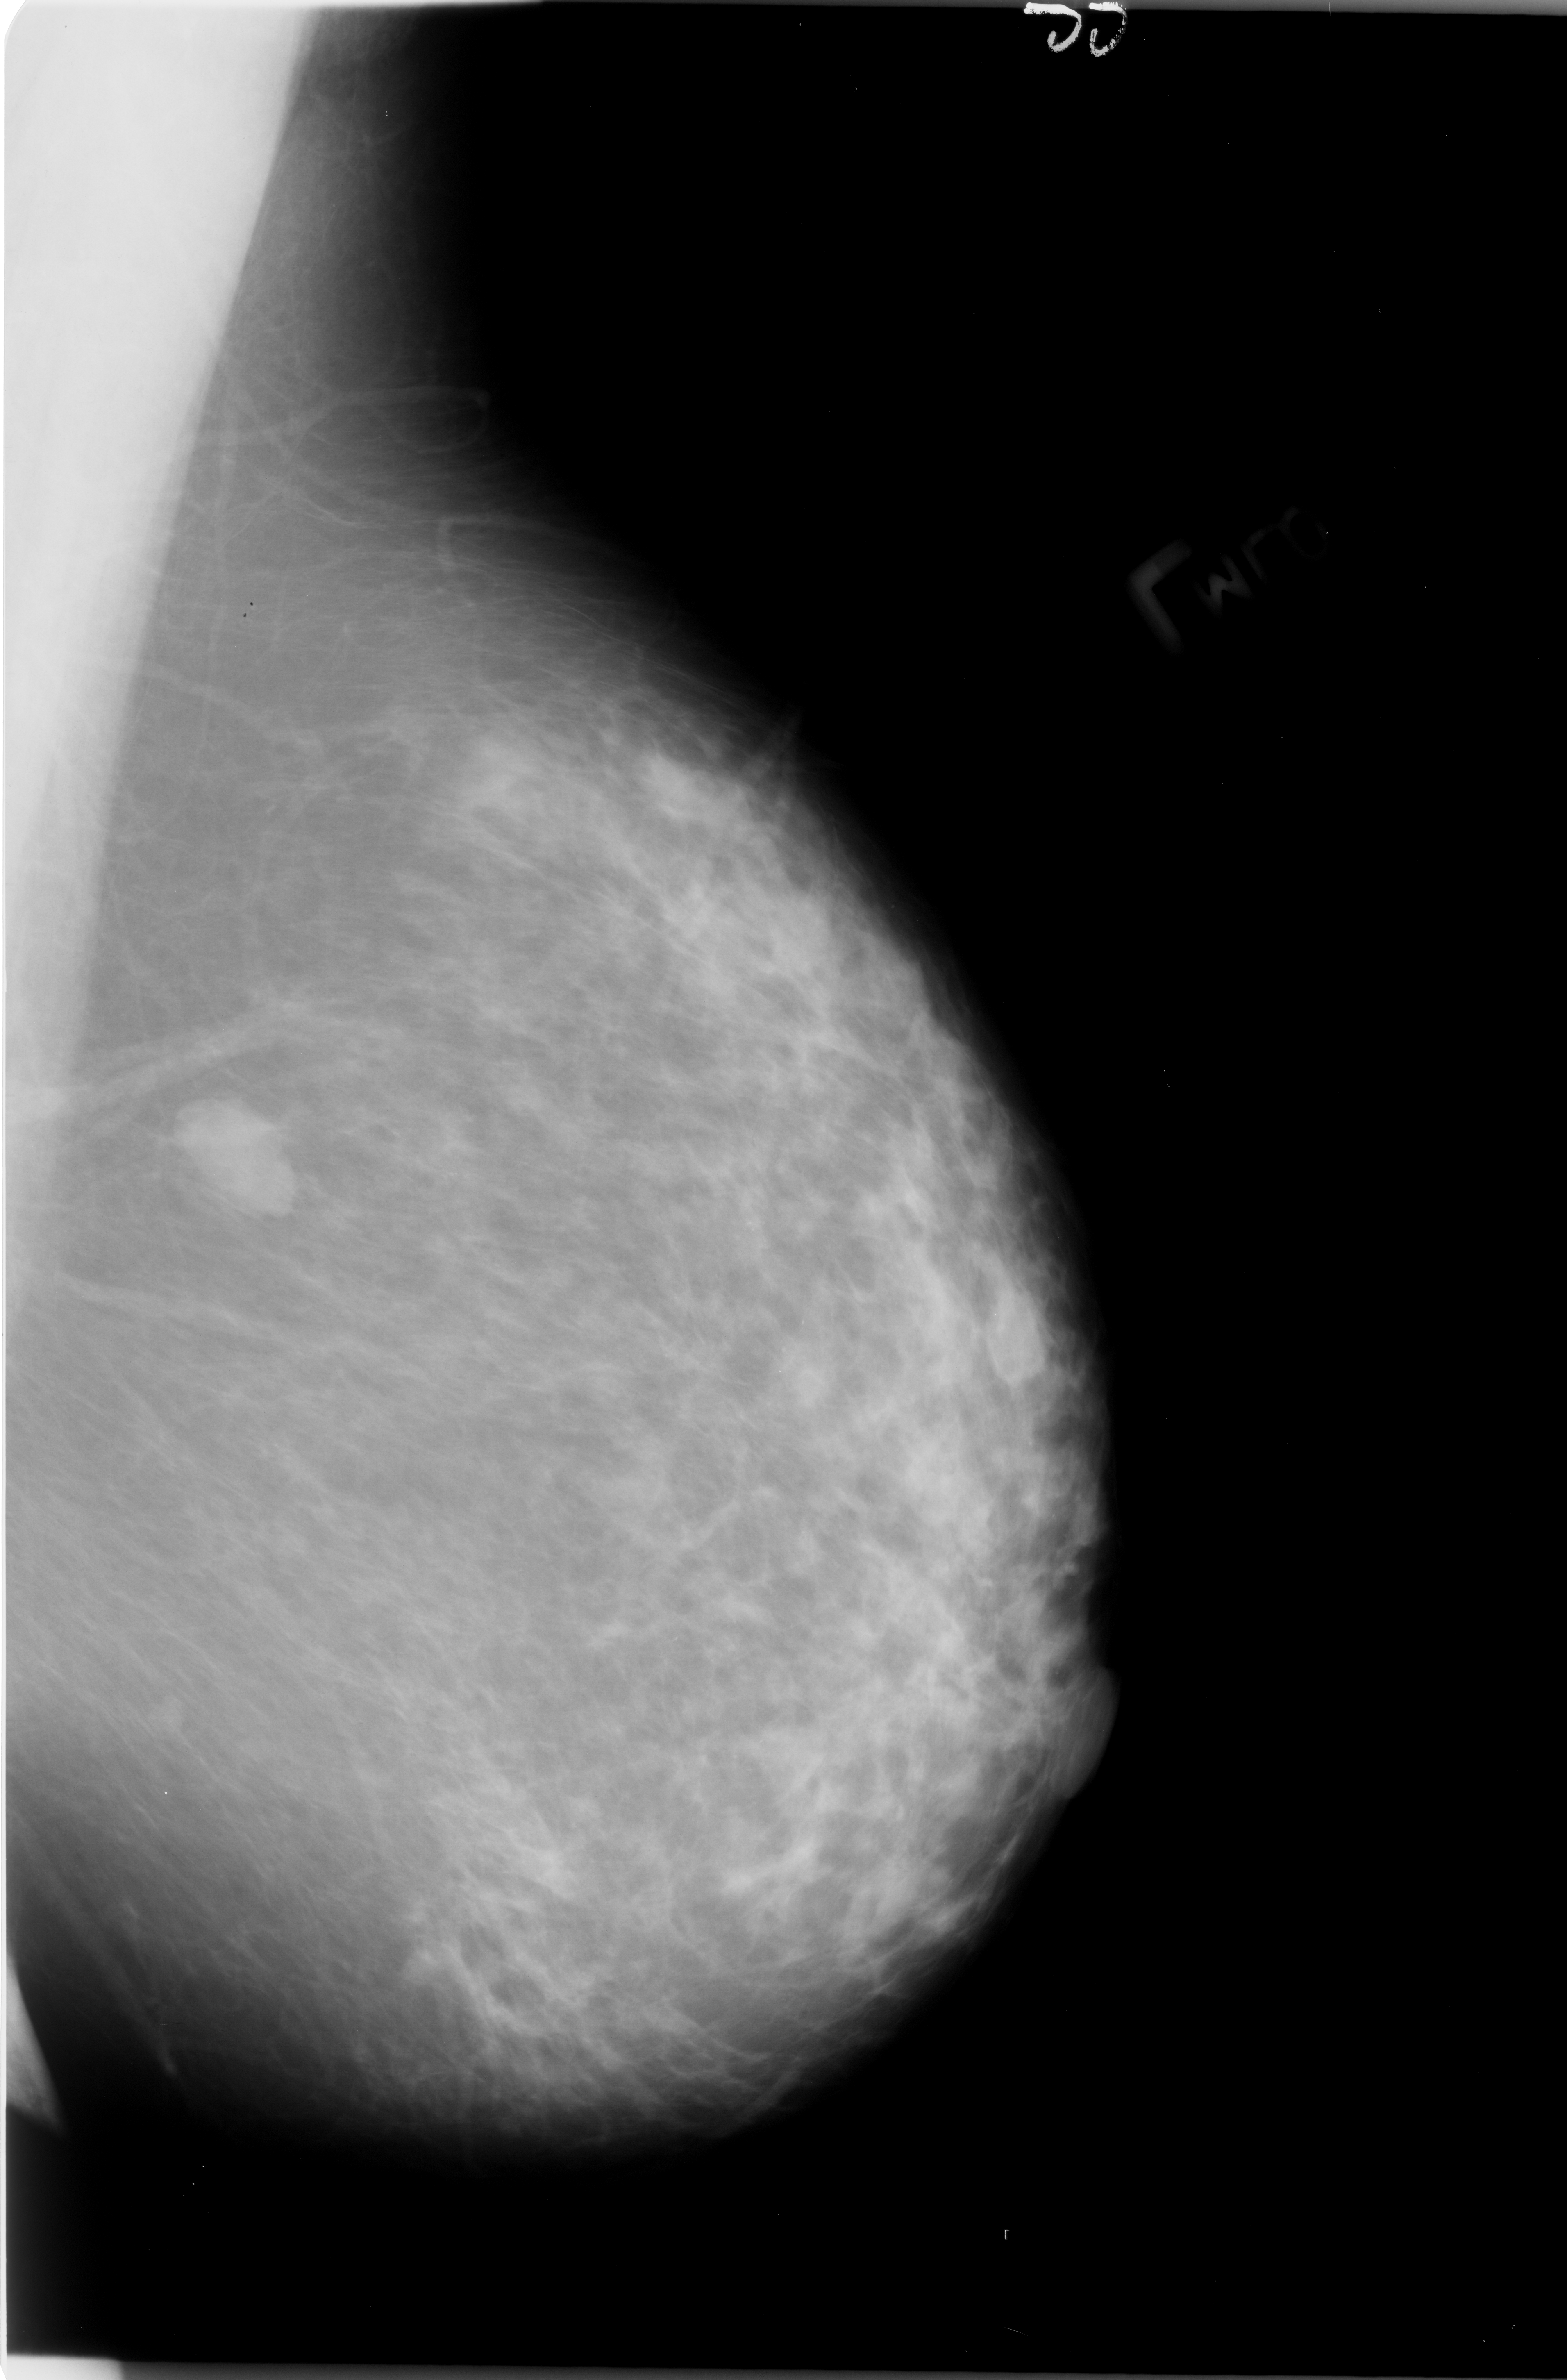
Mammogram (digitized film); left breast; MLO view.
- Finding: mass, shape lobulated / oval, margins circumscribed; BI-RADS assessment category 4; subtlety rating 5 on a 1 (subtle) to 5 (obvious) scale; pathology (as recorded): benign.